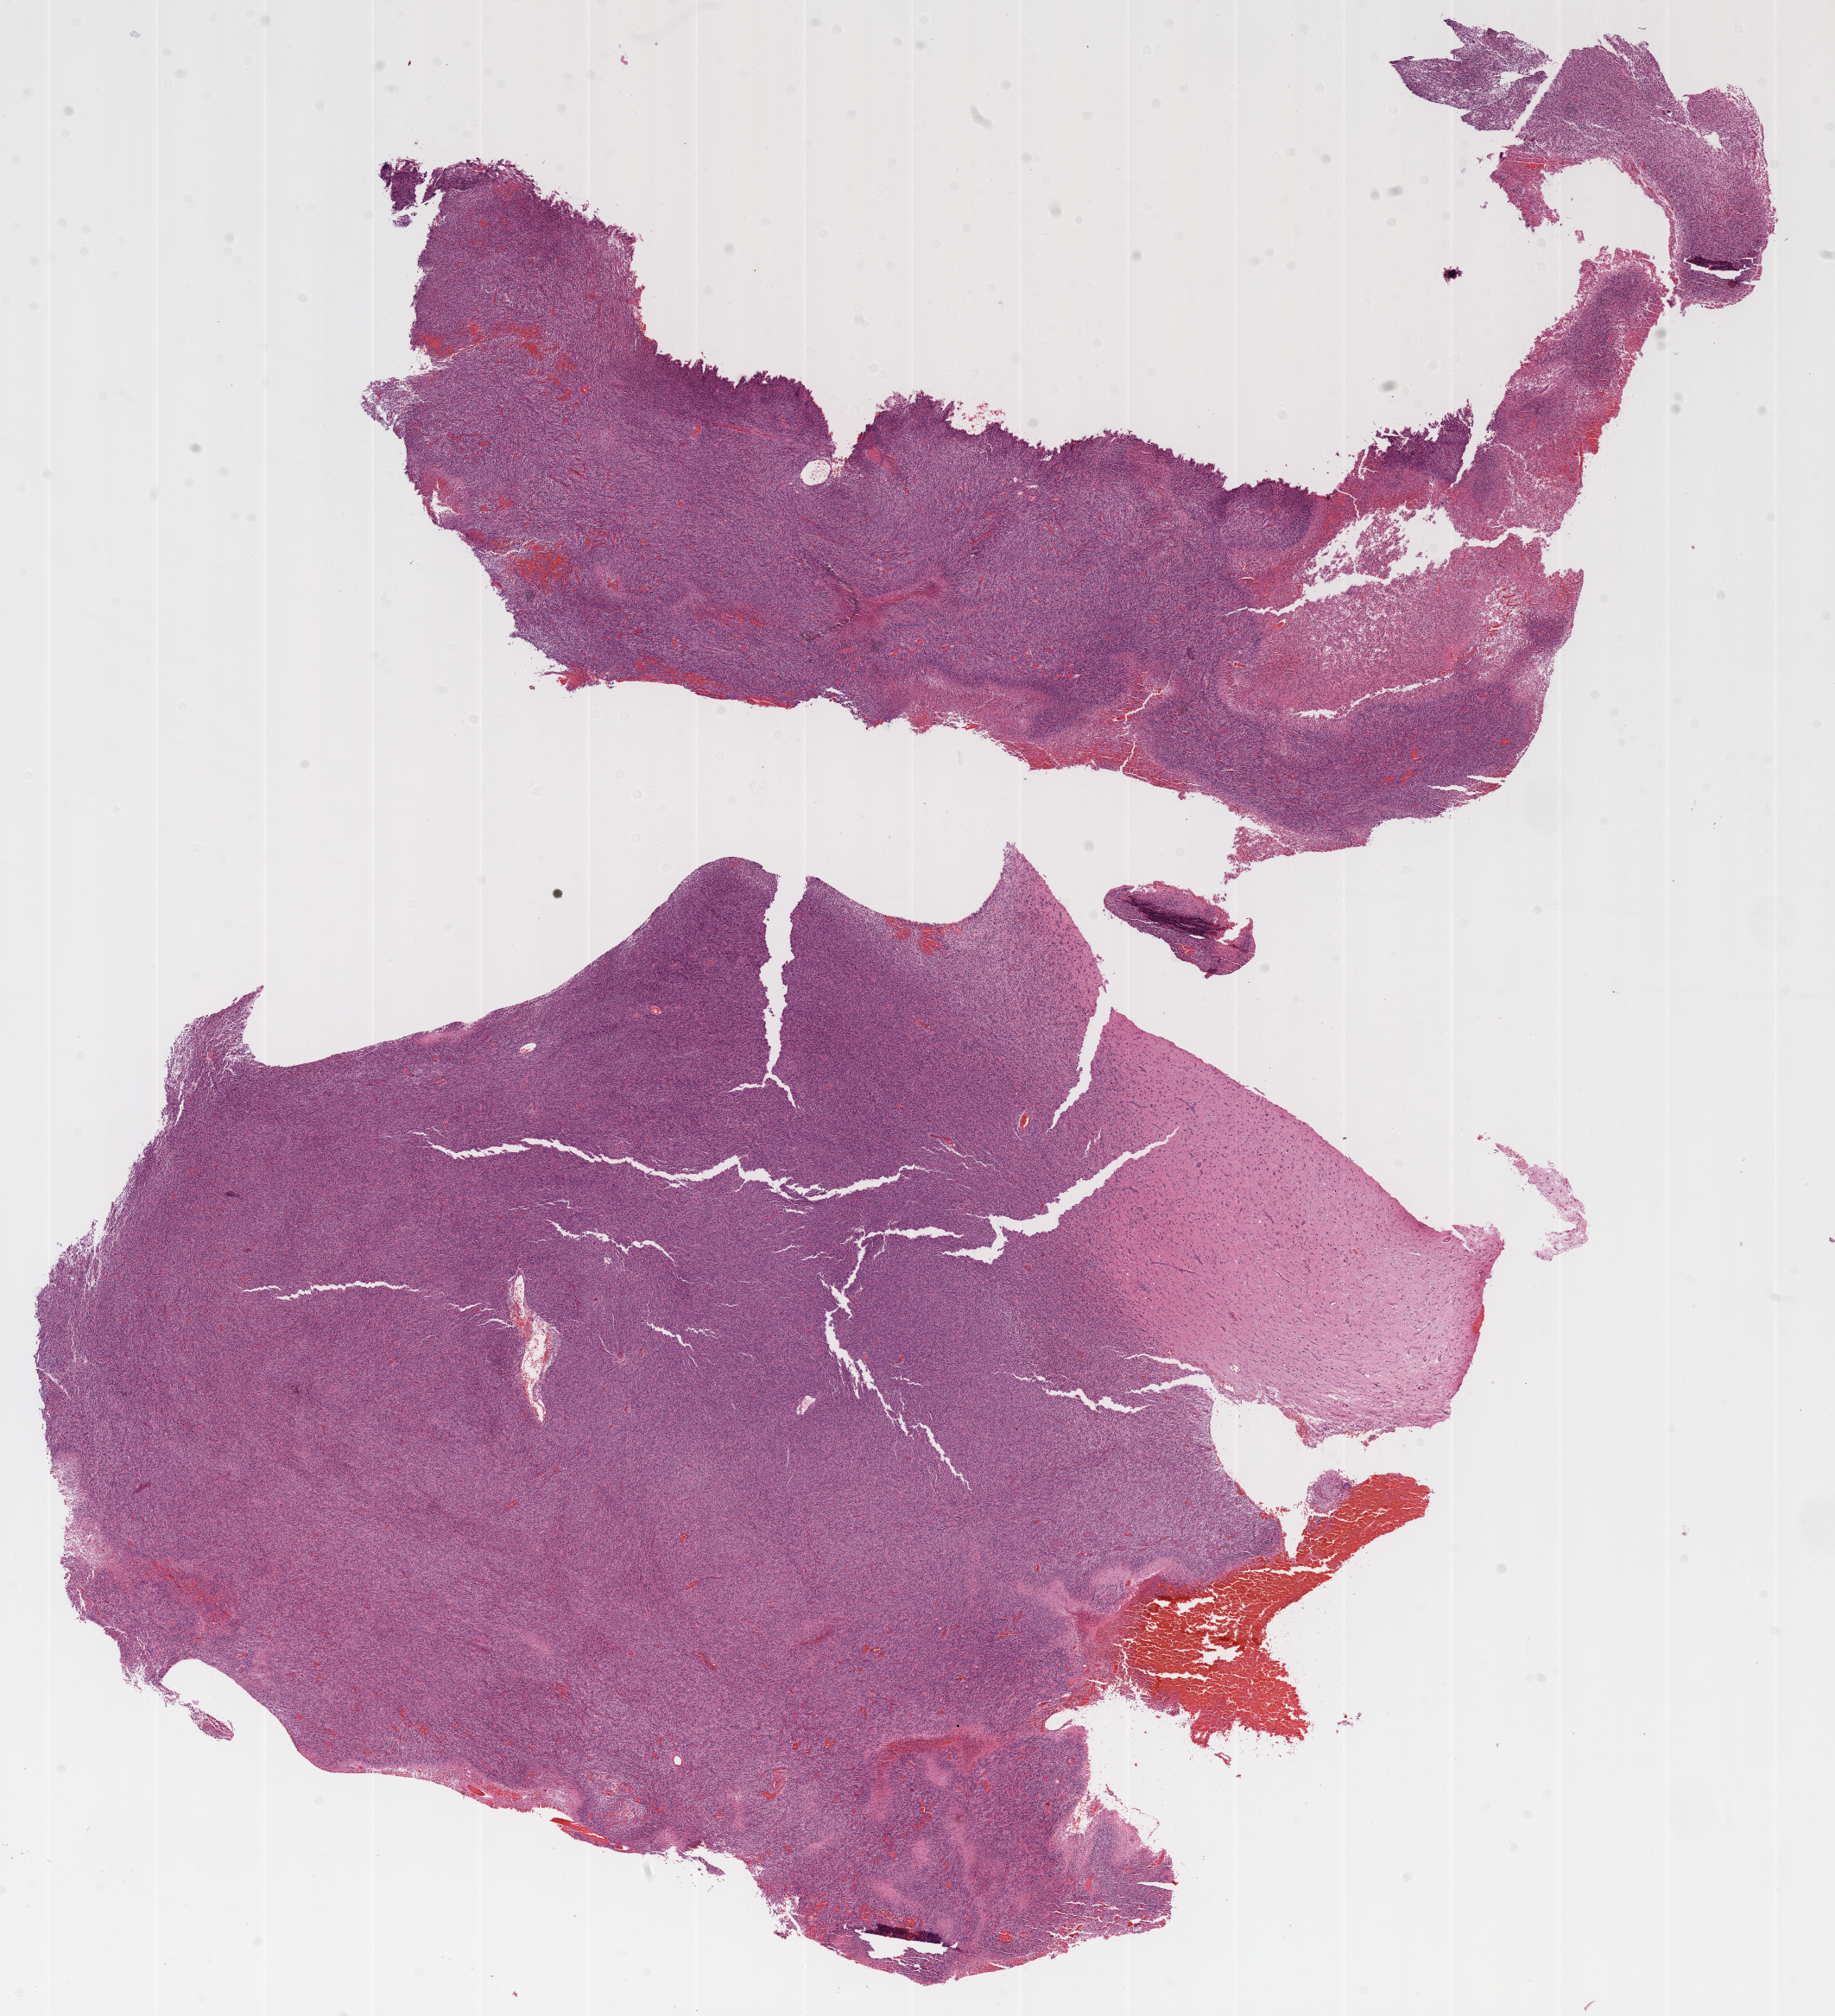
Digitized H&E tissue section (whole slide), whole scanned area (about 17.1 x 18.7 mm, slide scanned at 20x) shown as a low-resolution overview; formalin-fixed paraffin-embedded (FFPE) diagnostic section; brain, primary tumour sample. Female patient; age at initial diagnosis 53 years.
Histologic diagnosis: Glioblastoma.